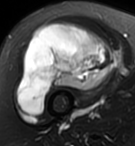
MRI of an extremity soft-tissue mass, one axial slice; slice 61 of 95 in the series (ordered by position); T2-weighted fat-saturated; MR volume resampled by the dataset authors to the PET/CT grid (not the native acquisition matrix); 3.27 mm slice thickness; 135 × 146 image matrix. Female patient. From the clinical record (not read from this slice): histological type: pleiomorphic undifferentiated sarcoma; grade: high; site of the primary tumour: right quadricep.
Structures marked on this image (expert contour drawn on MRI and transferred to this co-registered scan by the dataset authors):
- gross tumour volume including surrounding oedema: bounding box [x1, y1, x2, y2] px = [16, 22, 116, 115]
- gross tumour volume (mass): [16, 22, 116, 115]